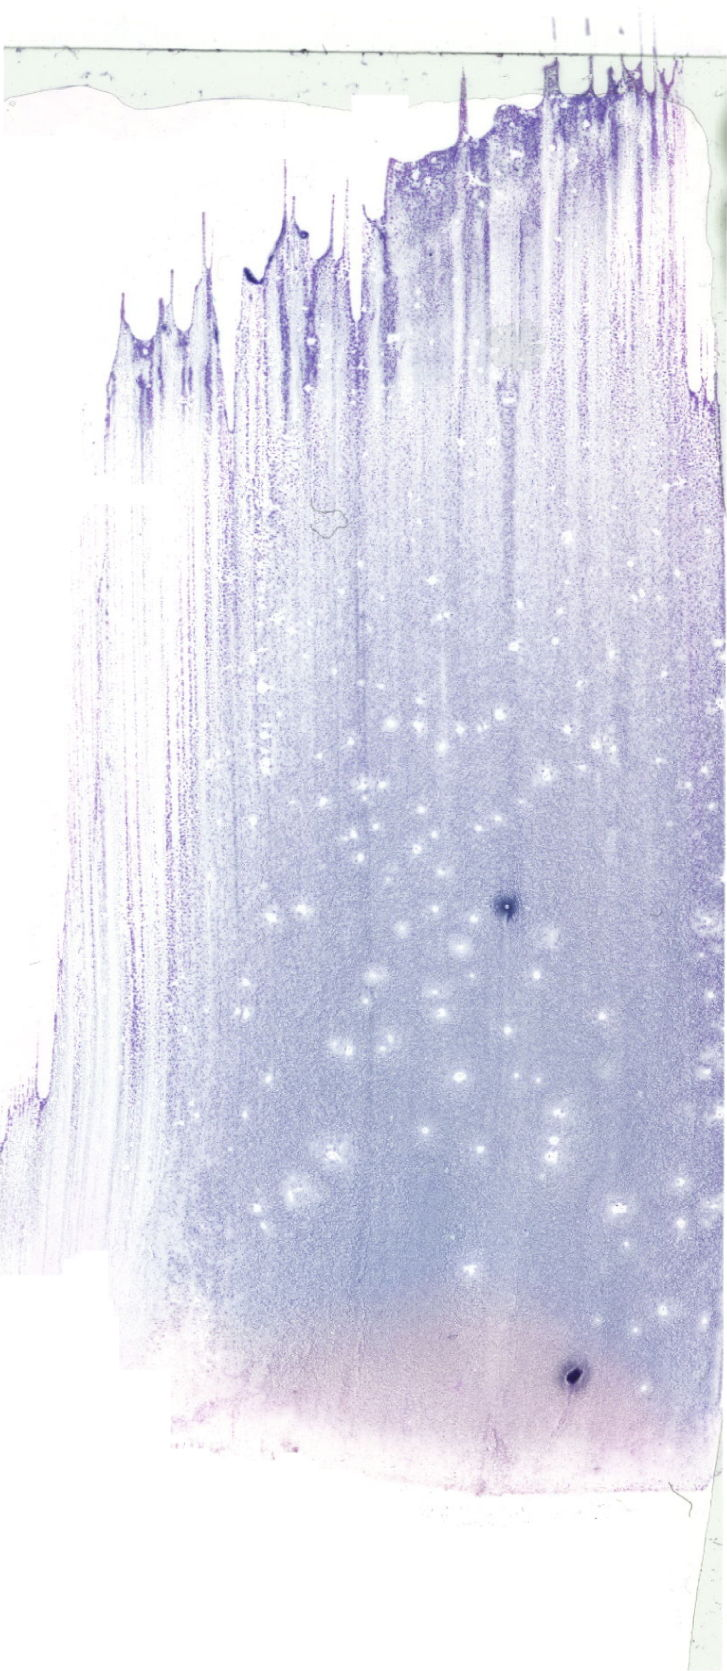
Bone marrow aspirate smear, May-Grünwald-Giemsa (MGG) stain, whole-slide image — shown as a low-resolution overview of the whole scanned area (about 20.6 x 47.4 mm). Patient sex: male.
* diagnosis: Acute Promyelocytic Leukemia with t(15;17)(q24.1;q21.2);PML-RARA